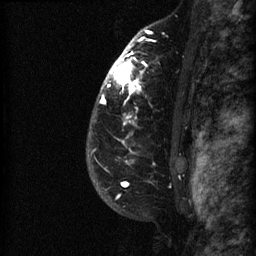
Breast MRI (dynamic contrast-enhanced), one sagittal slice. Dynamic contrast-enhanced series, image 2 of 3 at this slice position (ordered by acquisition). 1.5 T. TE 4.2 ms, TR 22.7 ms. 1.5 mm slice thickness. 256 × 256 image matrix, field of view 180 × 180 mm. Patient: female, 48 years. From the clinical record (not read from this slice): setting: breast cancer imaged before/during neoadjuvant chemotherapy; receptor status: triple-negative.
Outlined on this slice (semi-automatically segmented with operator editing):
- analysis volume of interest (the breast-tissue region the enhancement analysis was run in; not a lesion): bounding box (x1, y1, x2, y2) in pixels: (89, 27, 191, 180)
- tumour enhancement mask (voxels above the 90 % enhancement threshold inside the analysis volume of interest): (99, 30, 152, 119)